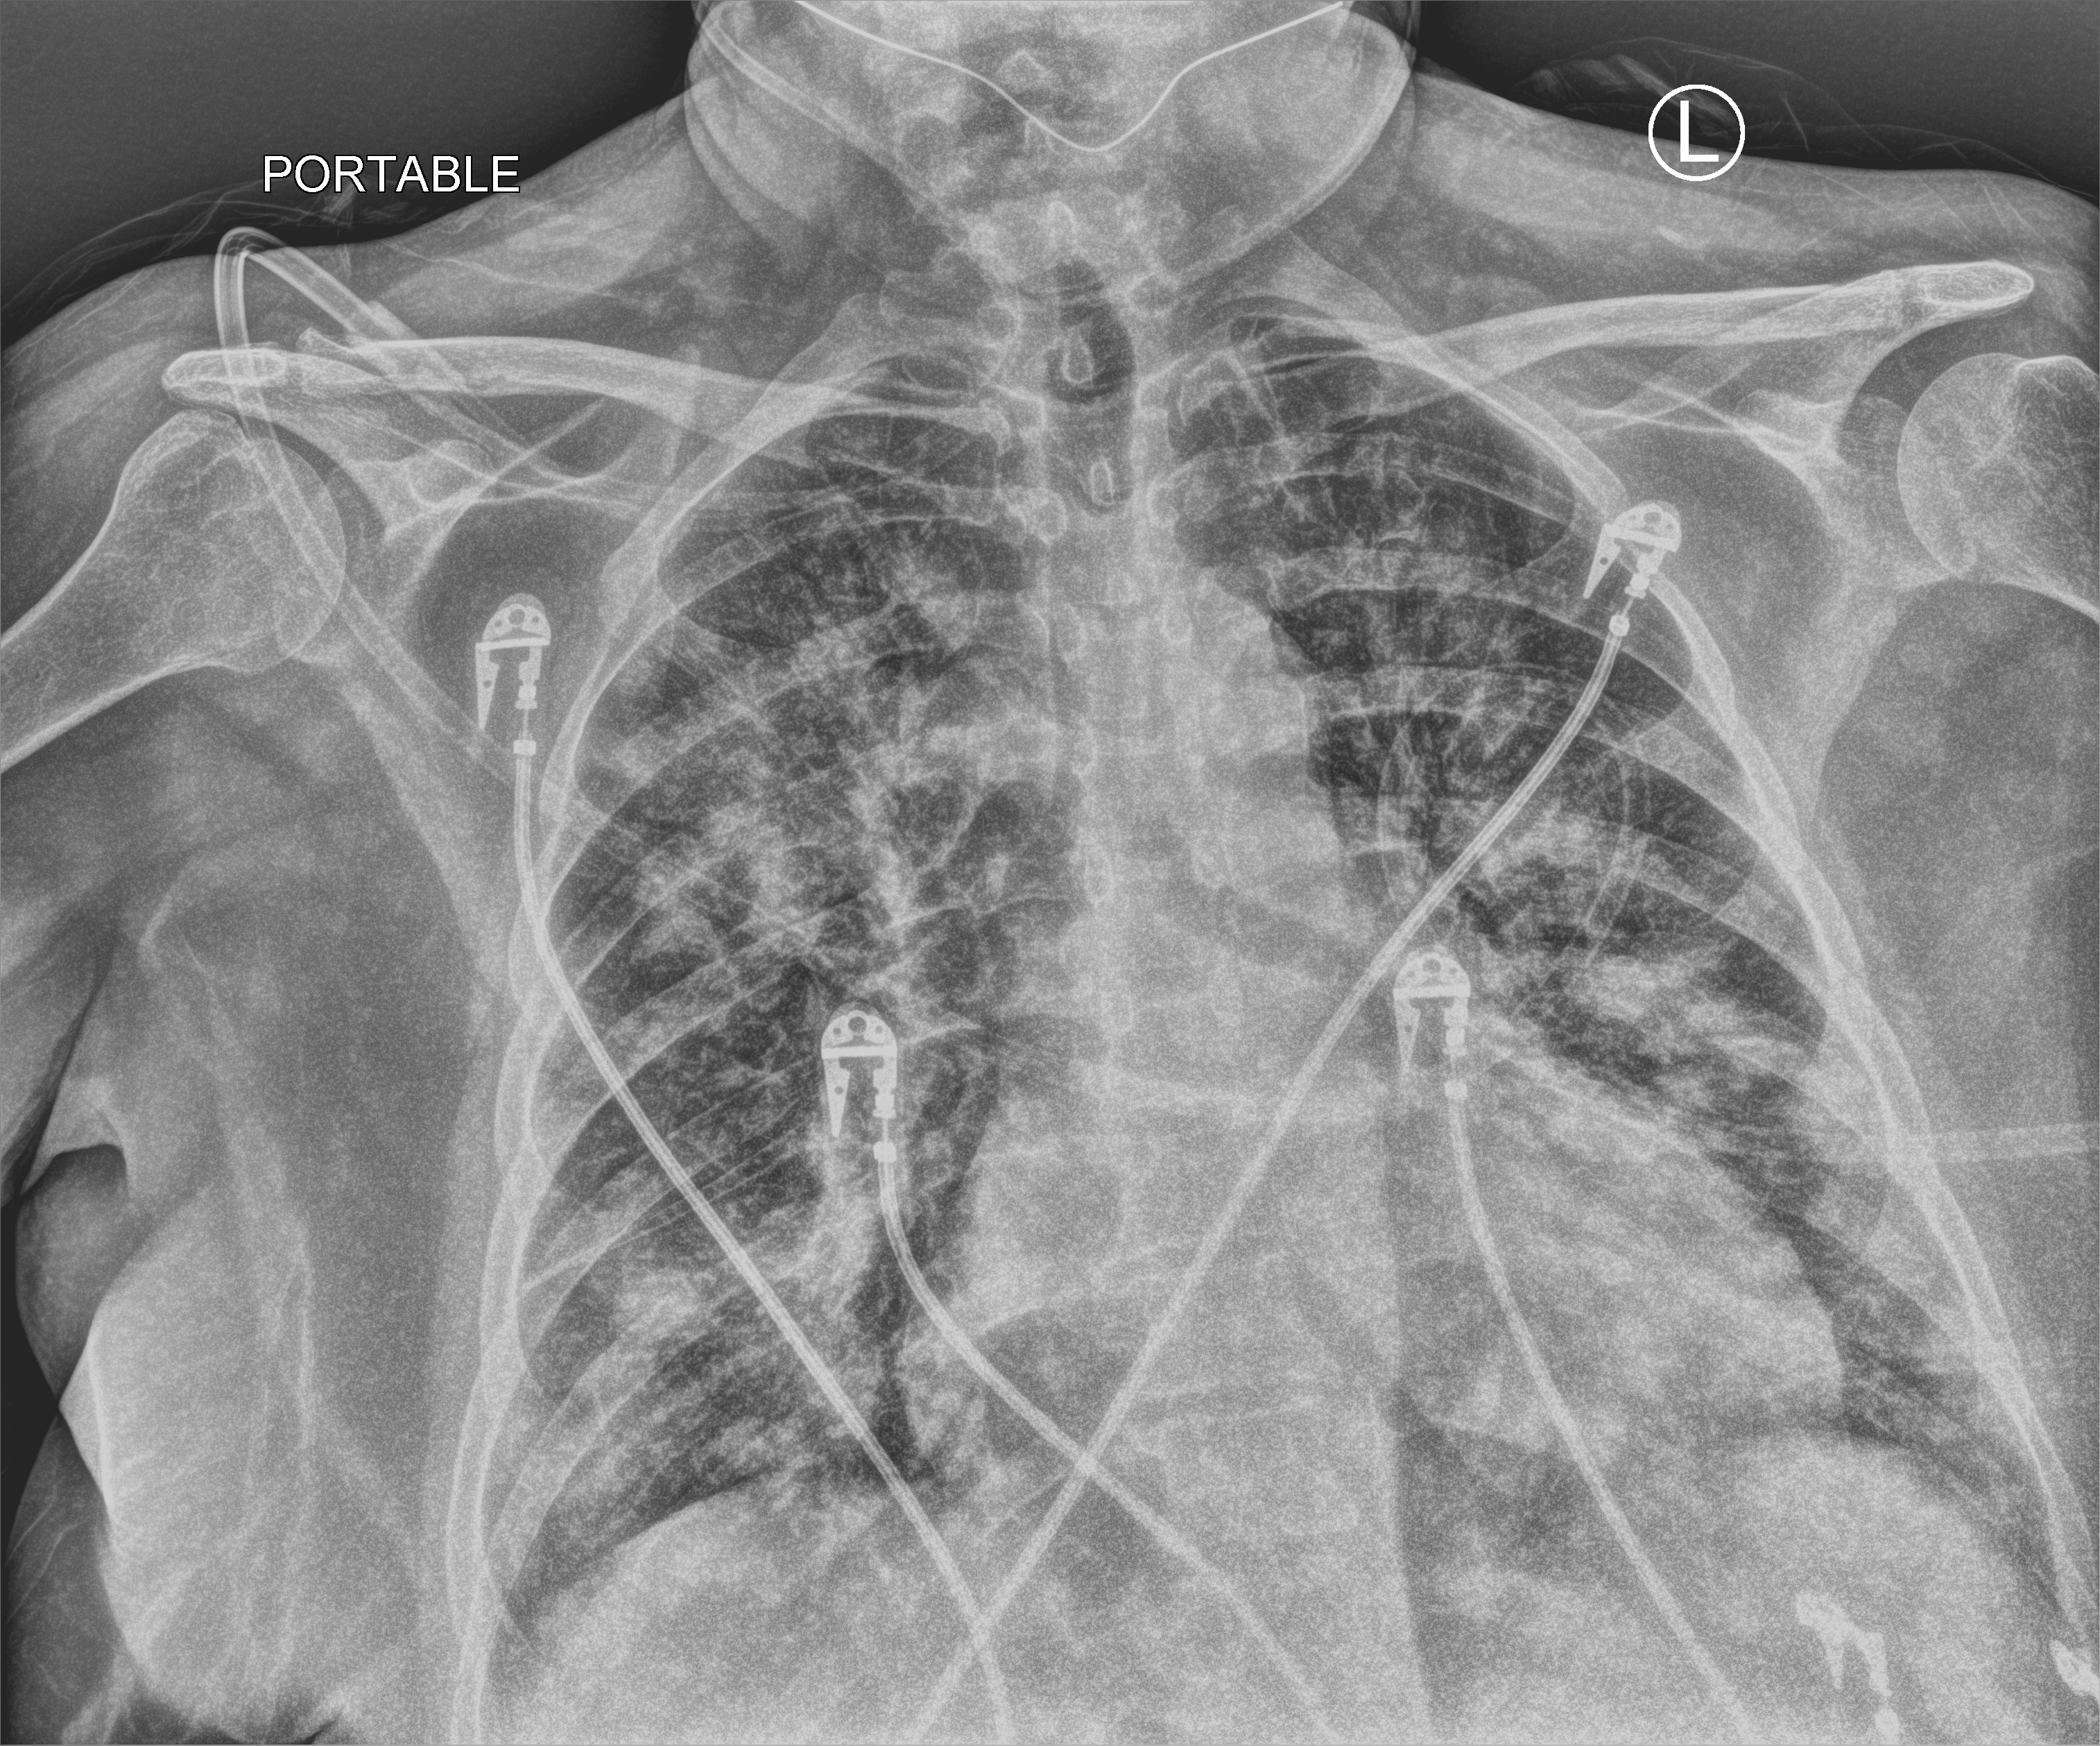
Bedside chest radiograph (computed radiography); anteroposterior (AP) projection. Patient hospitalised with COVID-19; female, aged 60–74 years.
From the hospital-stay record, not from the radiograph (when in the stay this image was taken is not recorded):
- mechanically ventilated during this hospital stay: no